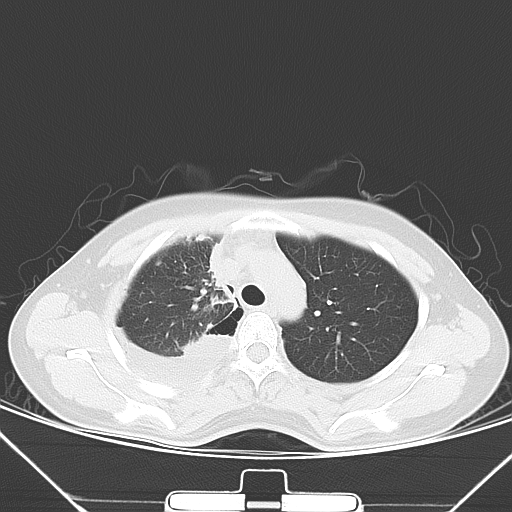
Chest CT, one axial slice; position 47 of 62 along the scan axis; lung window (W 1500 / L -600 HU); 5 mm slice thickness; 512 × 512 image matrix. Patient: female, 28 years. Case-level facts recorded for this patient, not image findings: clinical TNM (as recorded): T2 N0 M1a.
Annotated regions visible in this slice (bounding box drawn by a radiologist):
- lung tumour (recorded histology: adenocarcinoma): bounding box [x1, y1, x2, y2] px = [202, 242, 225, 299]